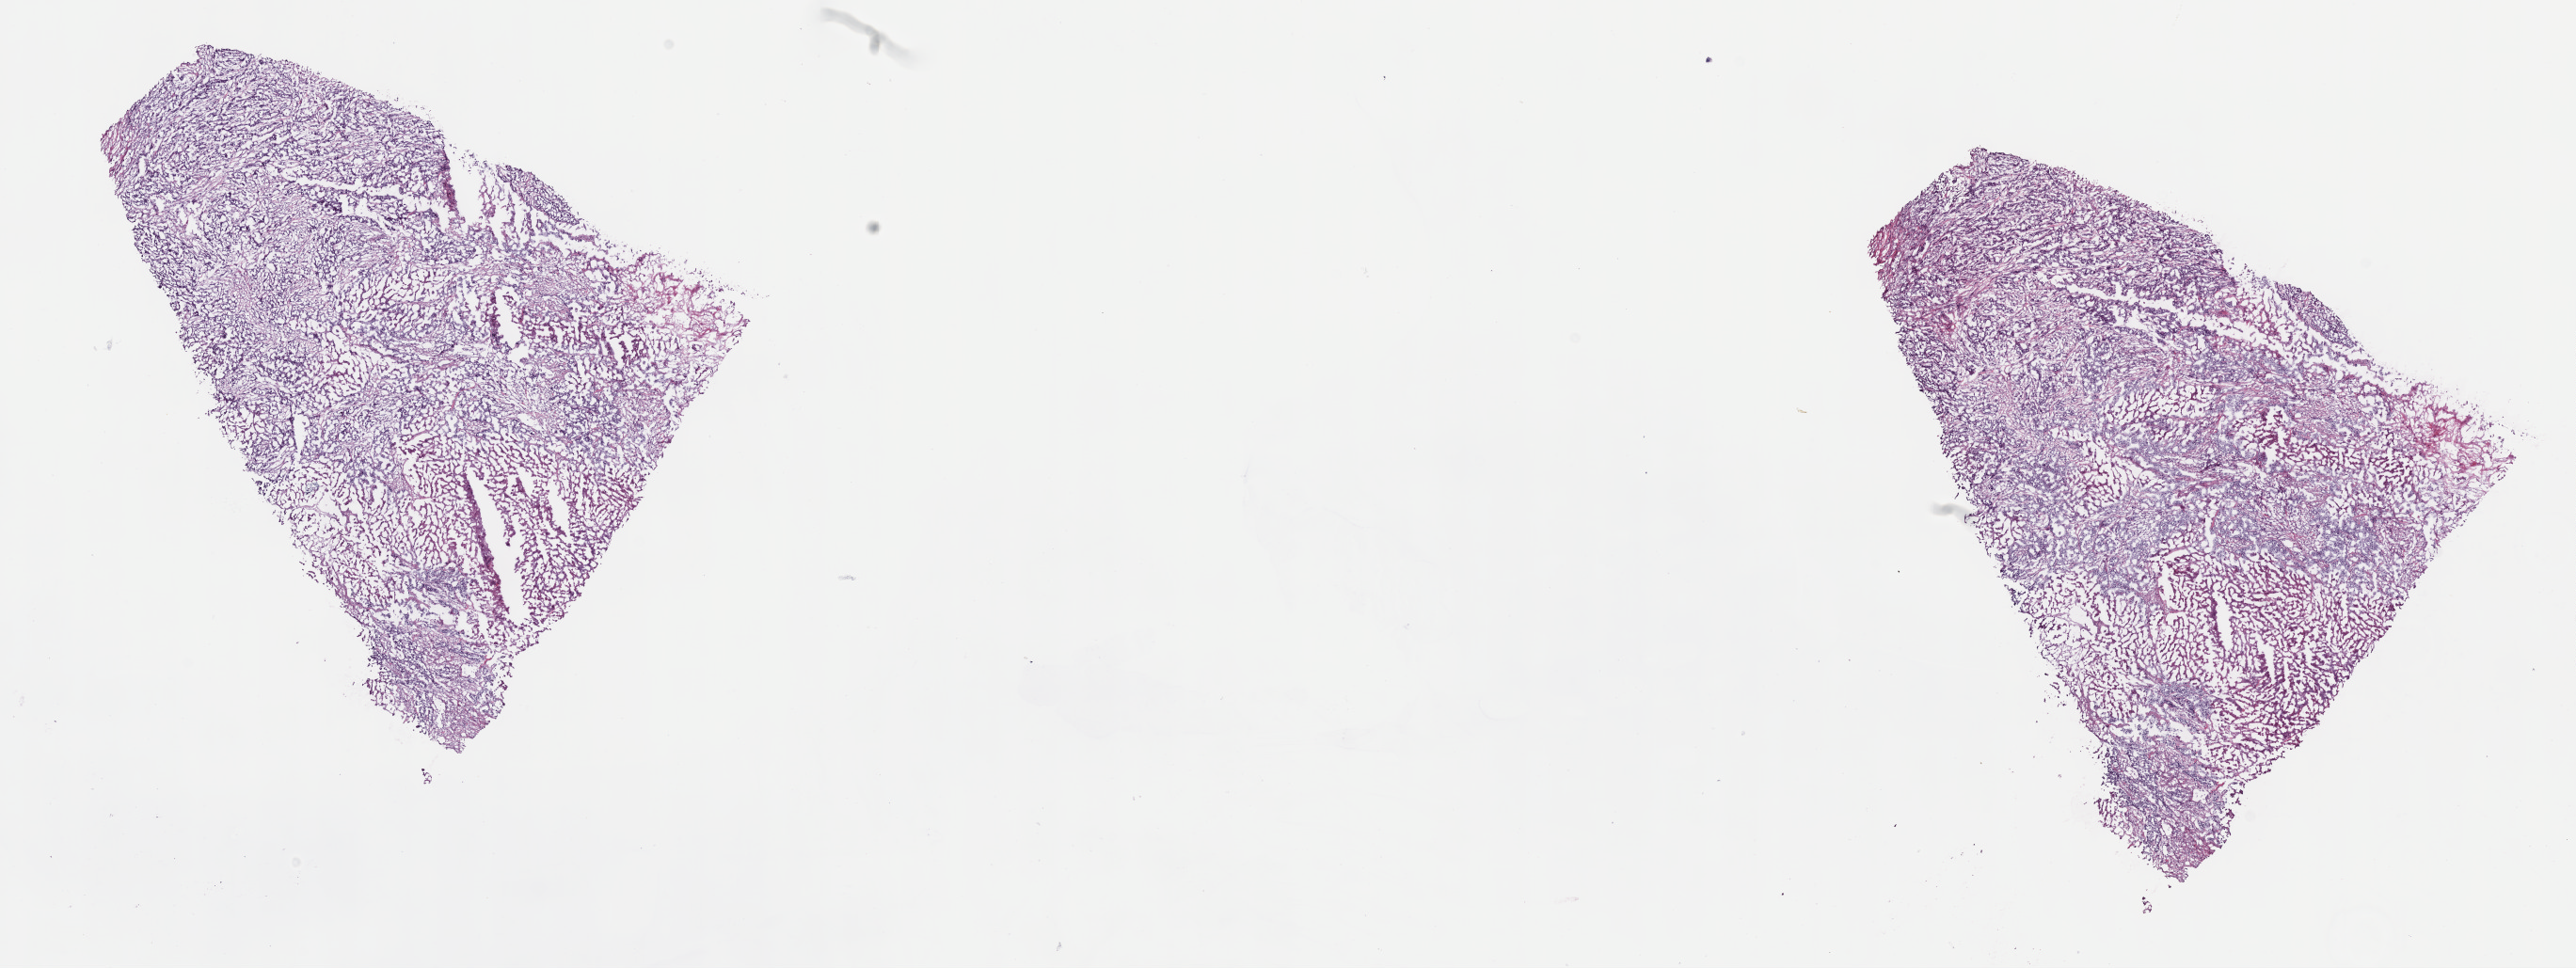
Whole-slide histology image, H&E-stained, low-resolution overview of the scanned area, about 22.1 x 8.3 mm. Frozen section. Lung, primary tumour sample. Male patient; age at initial diagnosis 61 years. Composition of this section per pathologist review: tumour cells 70%, tumour nuclei 70%, normal cells 0%, stromal cells 20%, necrosis 10%. Inflammatory infiltration, as recorded: lymphocyte infiltration 40%, monocyte infiltration 20%, neutrophil infiltration 20%.
AJCC pathologic stage: IIB. Diagnosis: Adenocarcinoma, NOS.